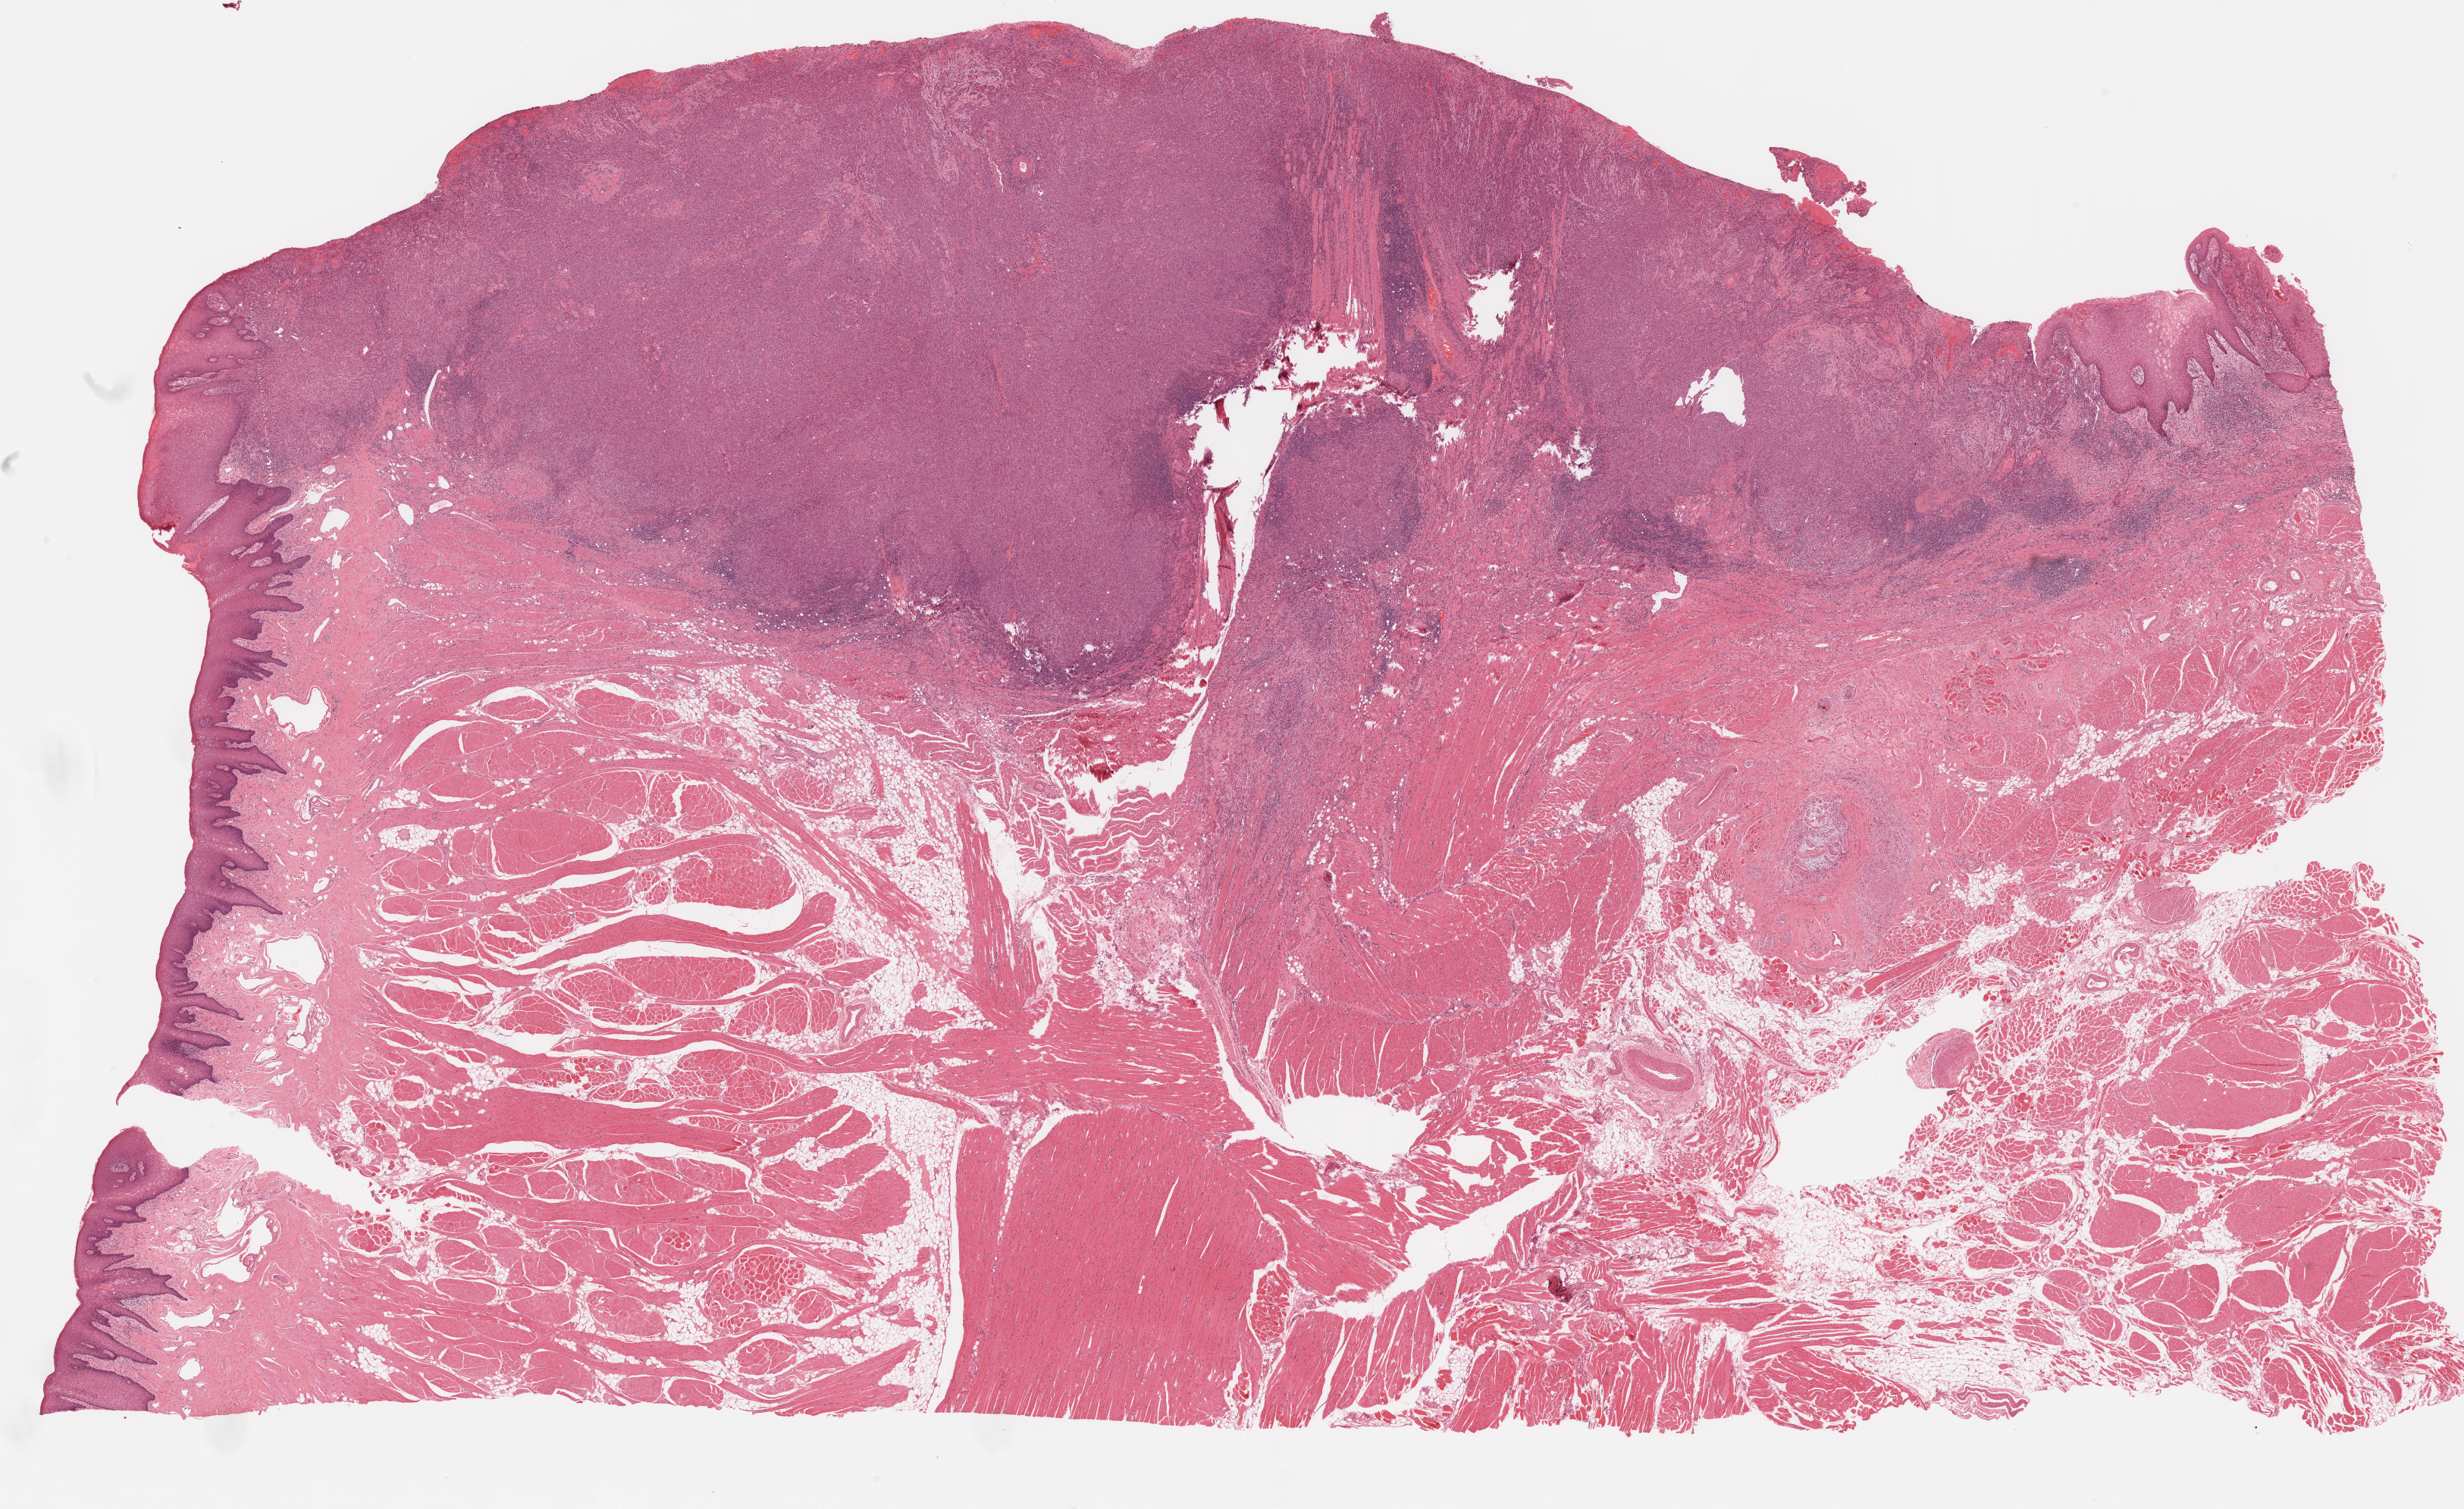
Whole-slide histology image, H&E-stained, whole scanned area (about 26.1 x 16.0 mm, from a 20x scan) shown as a low-resolution overview; formalin-fixed paraffin-embedded (FFPE) diagnostic section; head and neck, primary tumour sample. Male patient; age at initial diagnosis 74 years. Histologic grade: G3 (poorly differentiated).
TNM: T2 N0. Pathologic diagnosis: Squamous cell carcinoma, NOS. Lymph nodes positive (case pathology): 0 of 21 examined. AJCC pathologic stage: II.